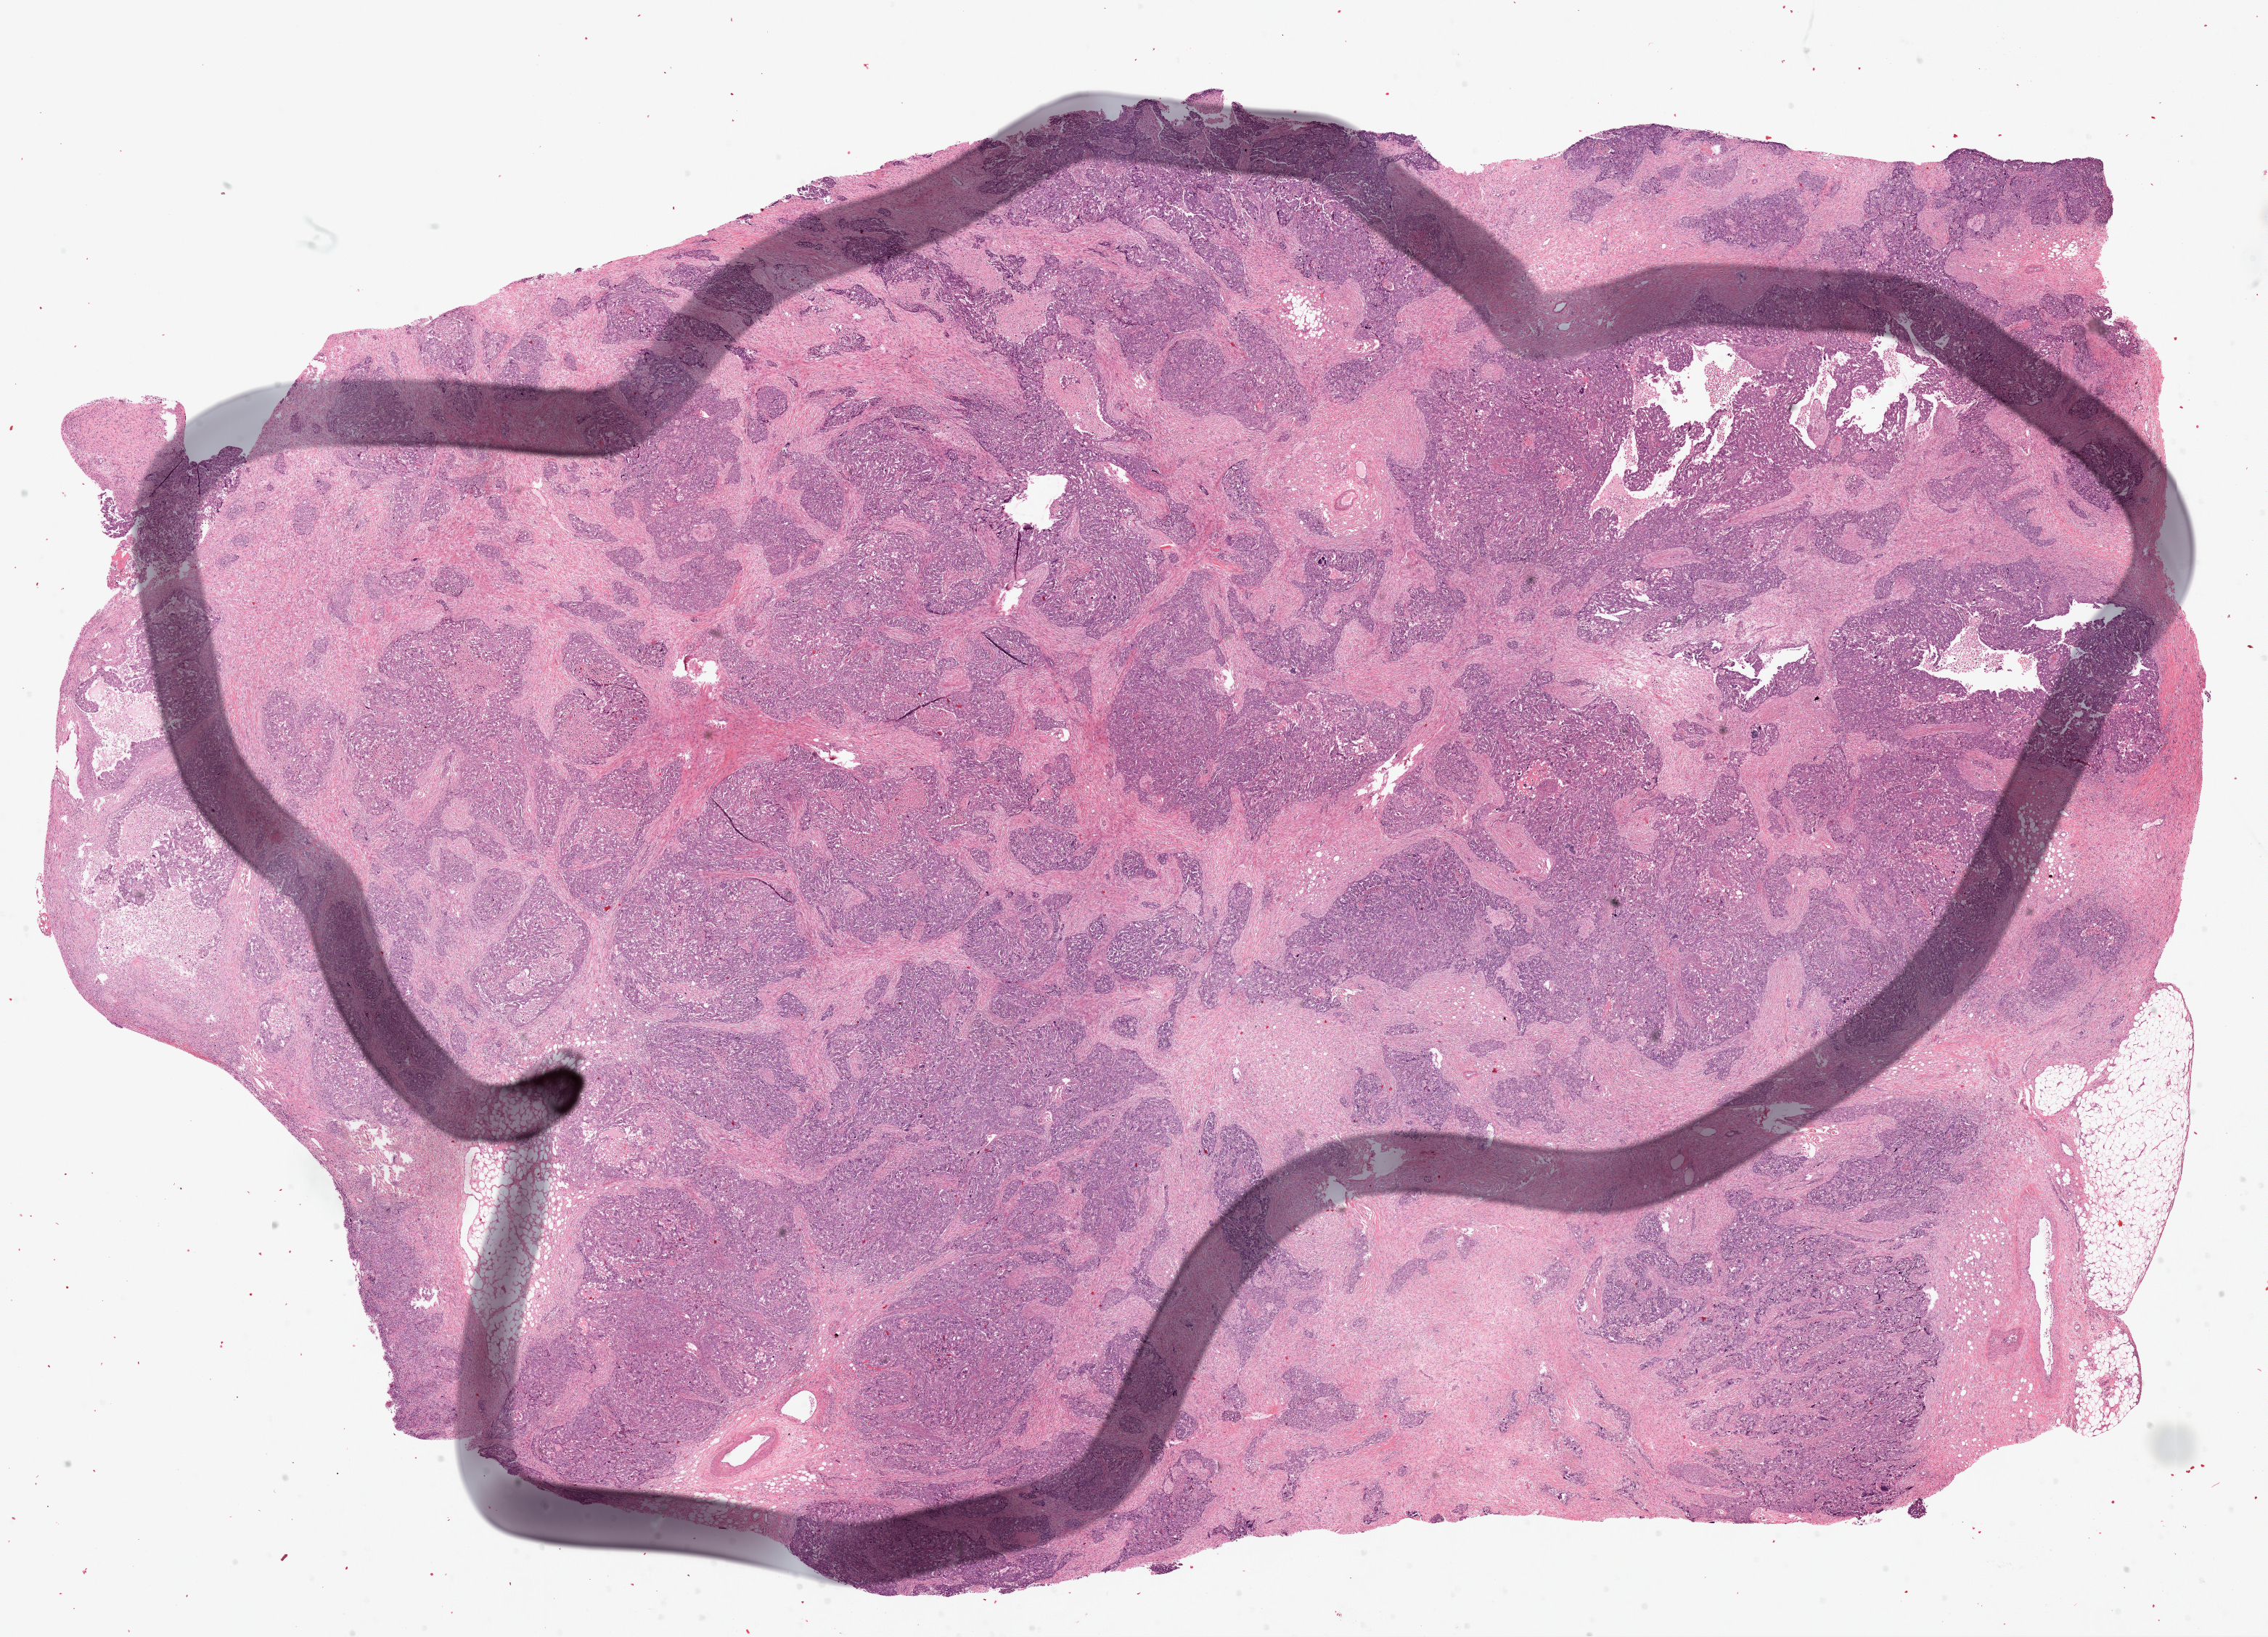
Whole-slide histology image, Hematoxylin and eosin (H&E) stained, low-resolution overview of the scanned area, about 25.1 x 18.1 mm. Frozen section from the top of the tissue portion. Ovary, primary tumour sample. Female patient; age at initial diagnosis 71 years.
Diagnosis: Serous cystadenocarcinoma, NOS (peritoneum, NOS).